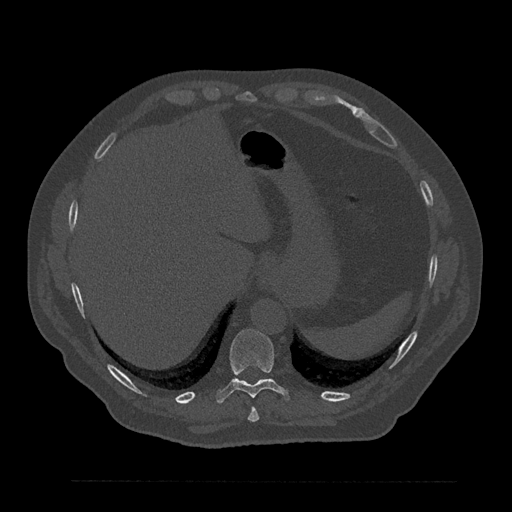
CT including the spine, one axial slice; position 350 of 797 along the scan axis; 120 kVp; bone window (W 1800 / L 400 HU); 512 × 512 image matrix, field of view 430 × 430 mm. Patient: male, 61 years. From the clinical record (not read from this slice): primary cancer: prostate.
Structures marked on this image (semi-automatic segmentation, software-assisted and operator-edited):
- T10 vertebra: bounding box <216,329,289,403> (left, top, right, bottom; pixels)
- T9 vertebra: <248,407,259,422>